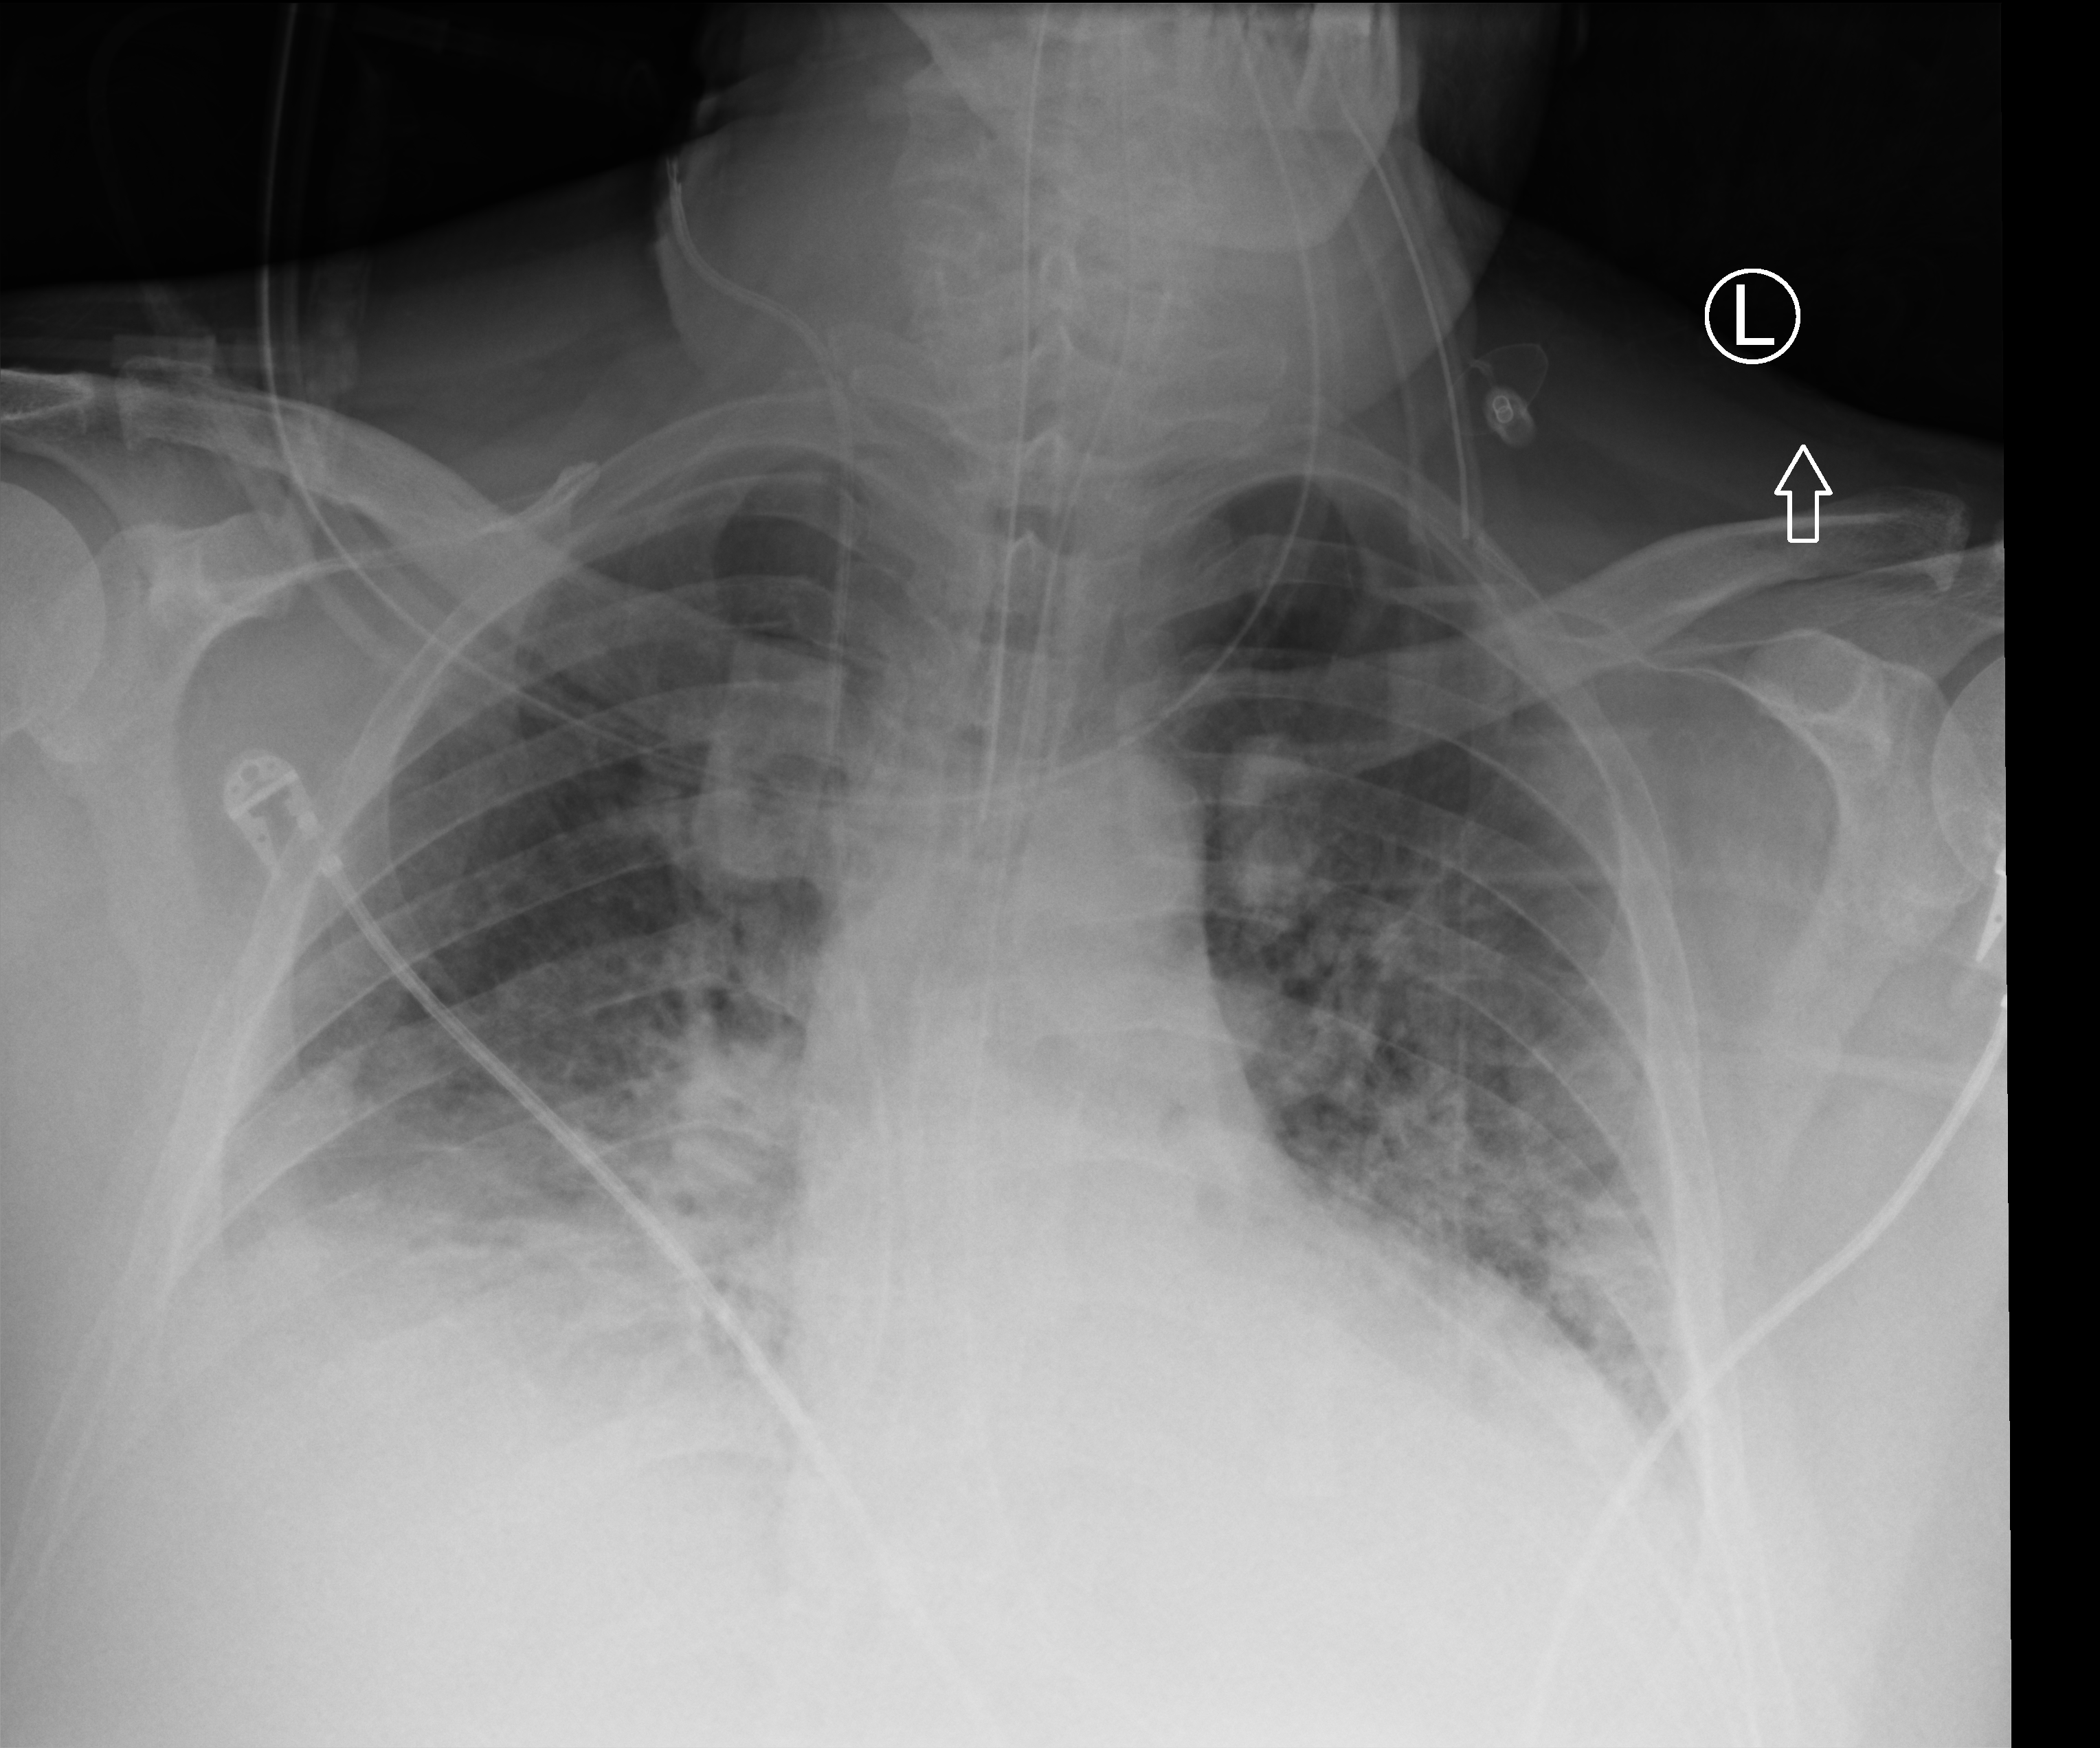
Portable chest radiograph. Male patient hospitalised with COVID-19, age 18–59 years.
Hospital-stay facts (about this admission, not read from this image; timing relative to this image not recorded):
- admitted to intensive care during this hospital stay: yes